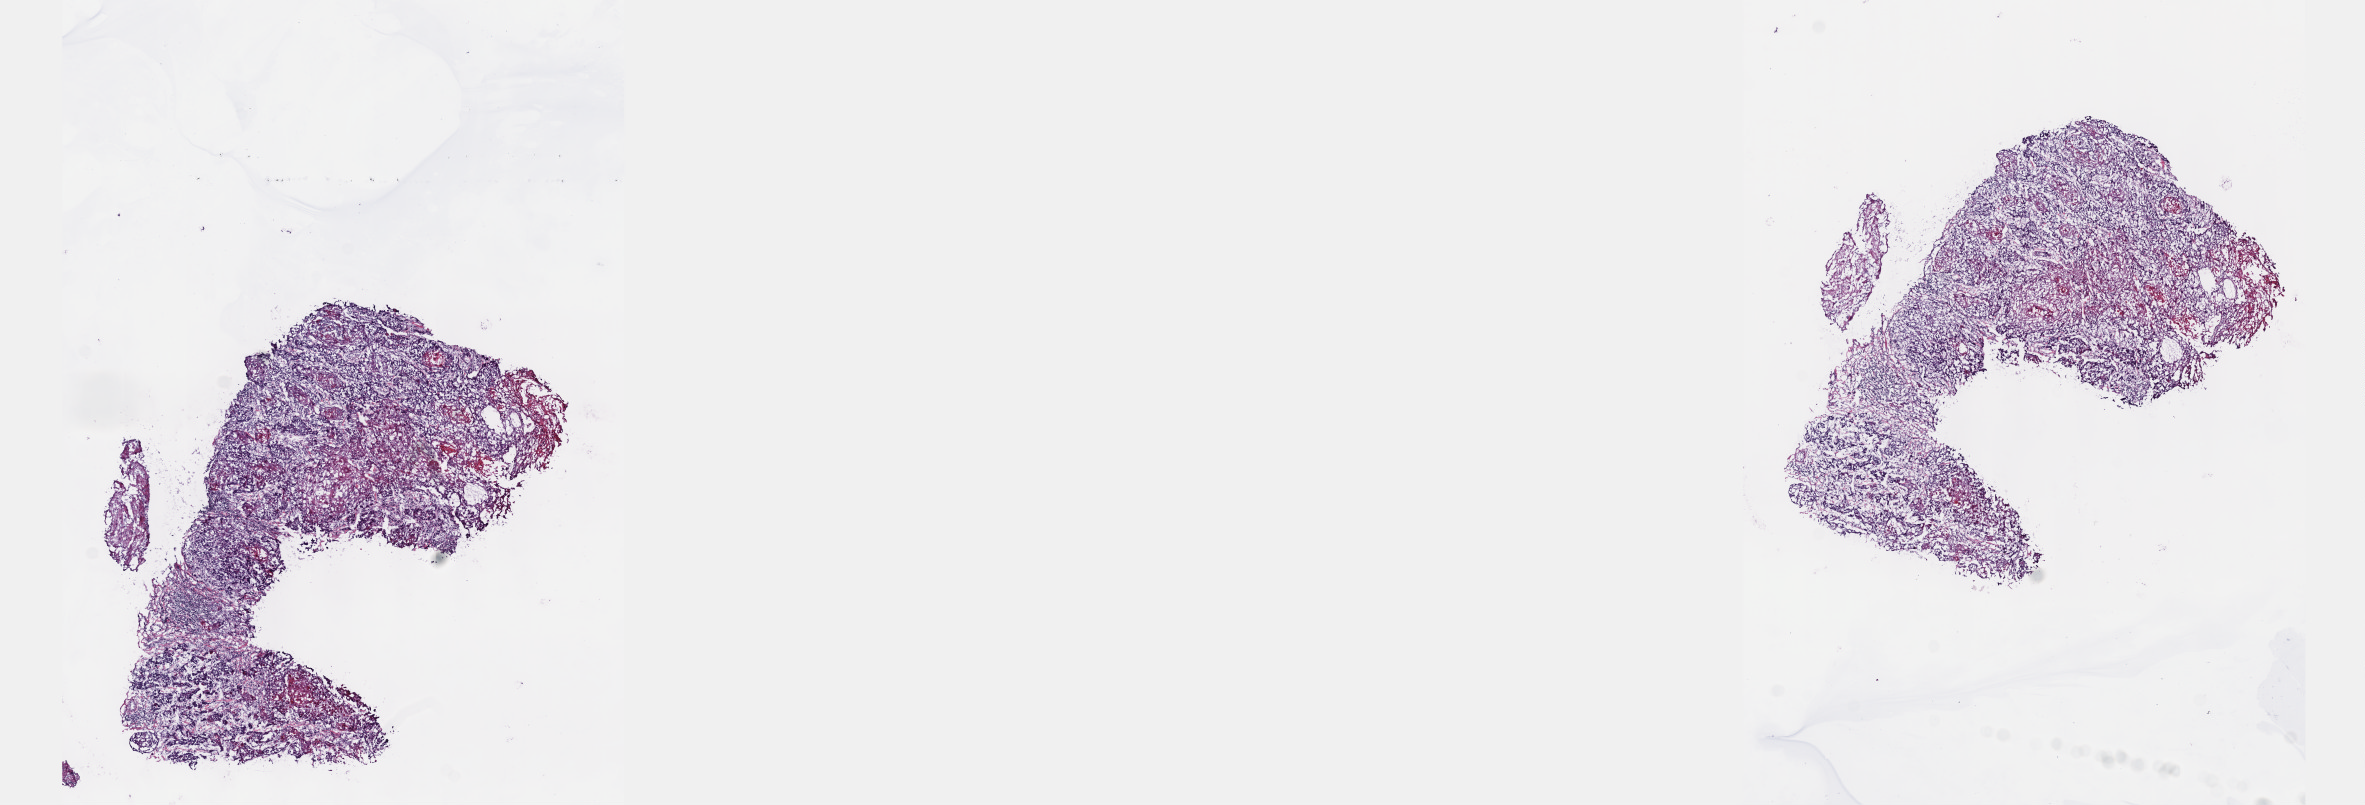
Digitized H&E-stained tissue section (whole slide) — shown as a low-resolution overview of the whole scanned area (about 19.1 x 6.5 mm, from a 40x scan); frozen section from the top of the tissue portion; primary tumour sample from the esophagus. Patient: male, age at initial diagnosis 51 years. Histologic grade: G2 (moderately differentiated). Pathologist review of this section (percent, as recorded): tumour cells 45%, tumour nuclei 60%, normal cells 0%, stromal cells 40%, necrosis 15%. Infiltration values recorded for this section: lymphocyte infiltration 40%, monocyte infiltration 2%, neutrophil infiltration 2%.
Lymph nodes positive (case pathology): 2 of 14 examined. Pathologic diagnosis: Squamous cell carcinoma, NOS (middle third of esophagus). AJCC pathologic stage: IV (7th edition).